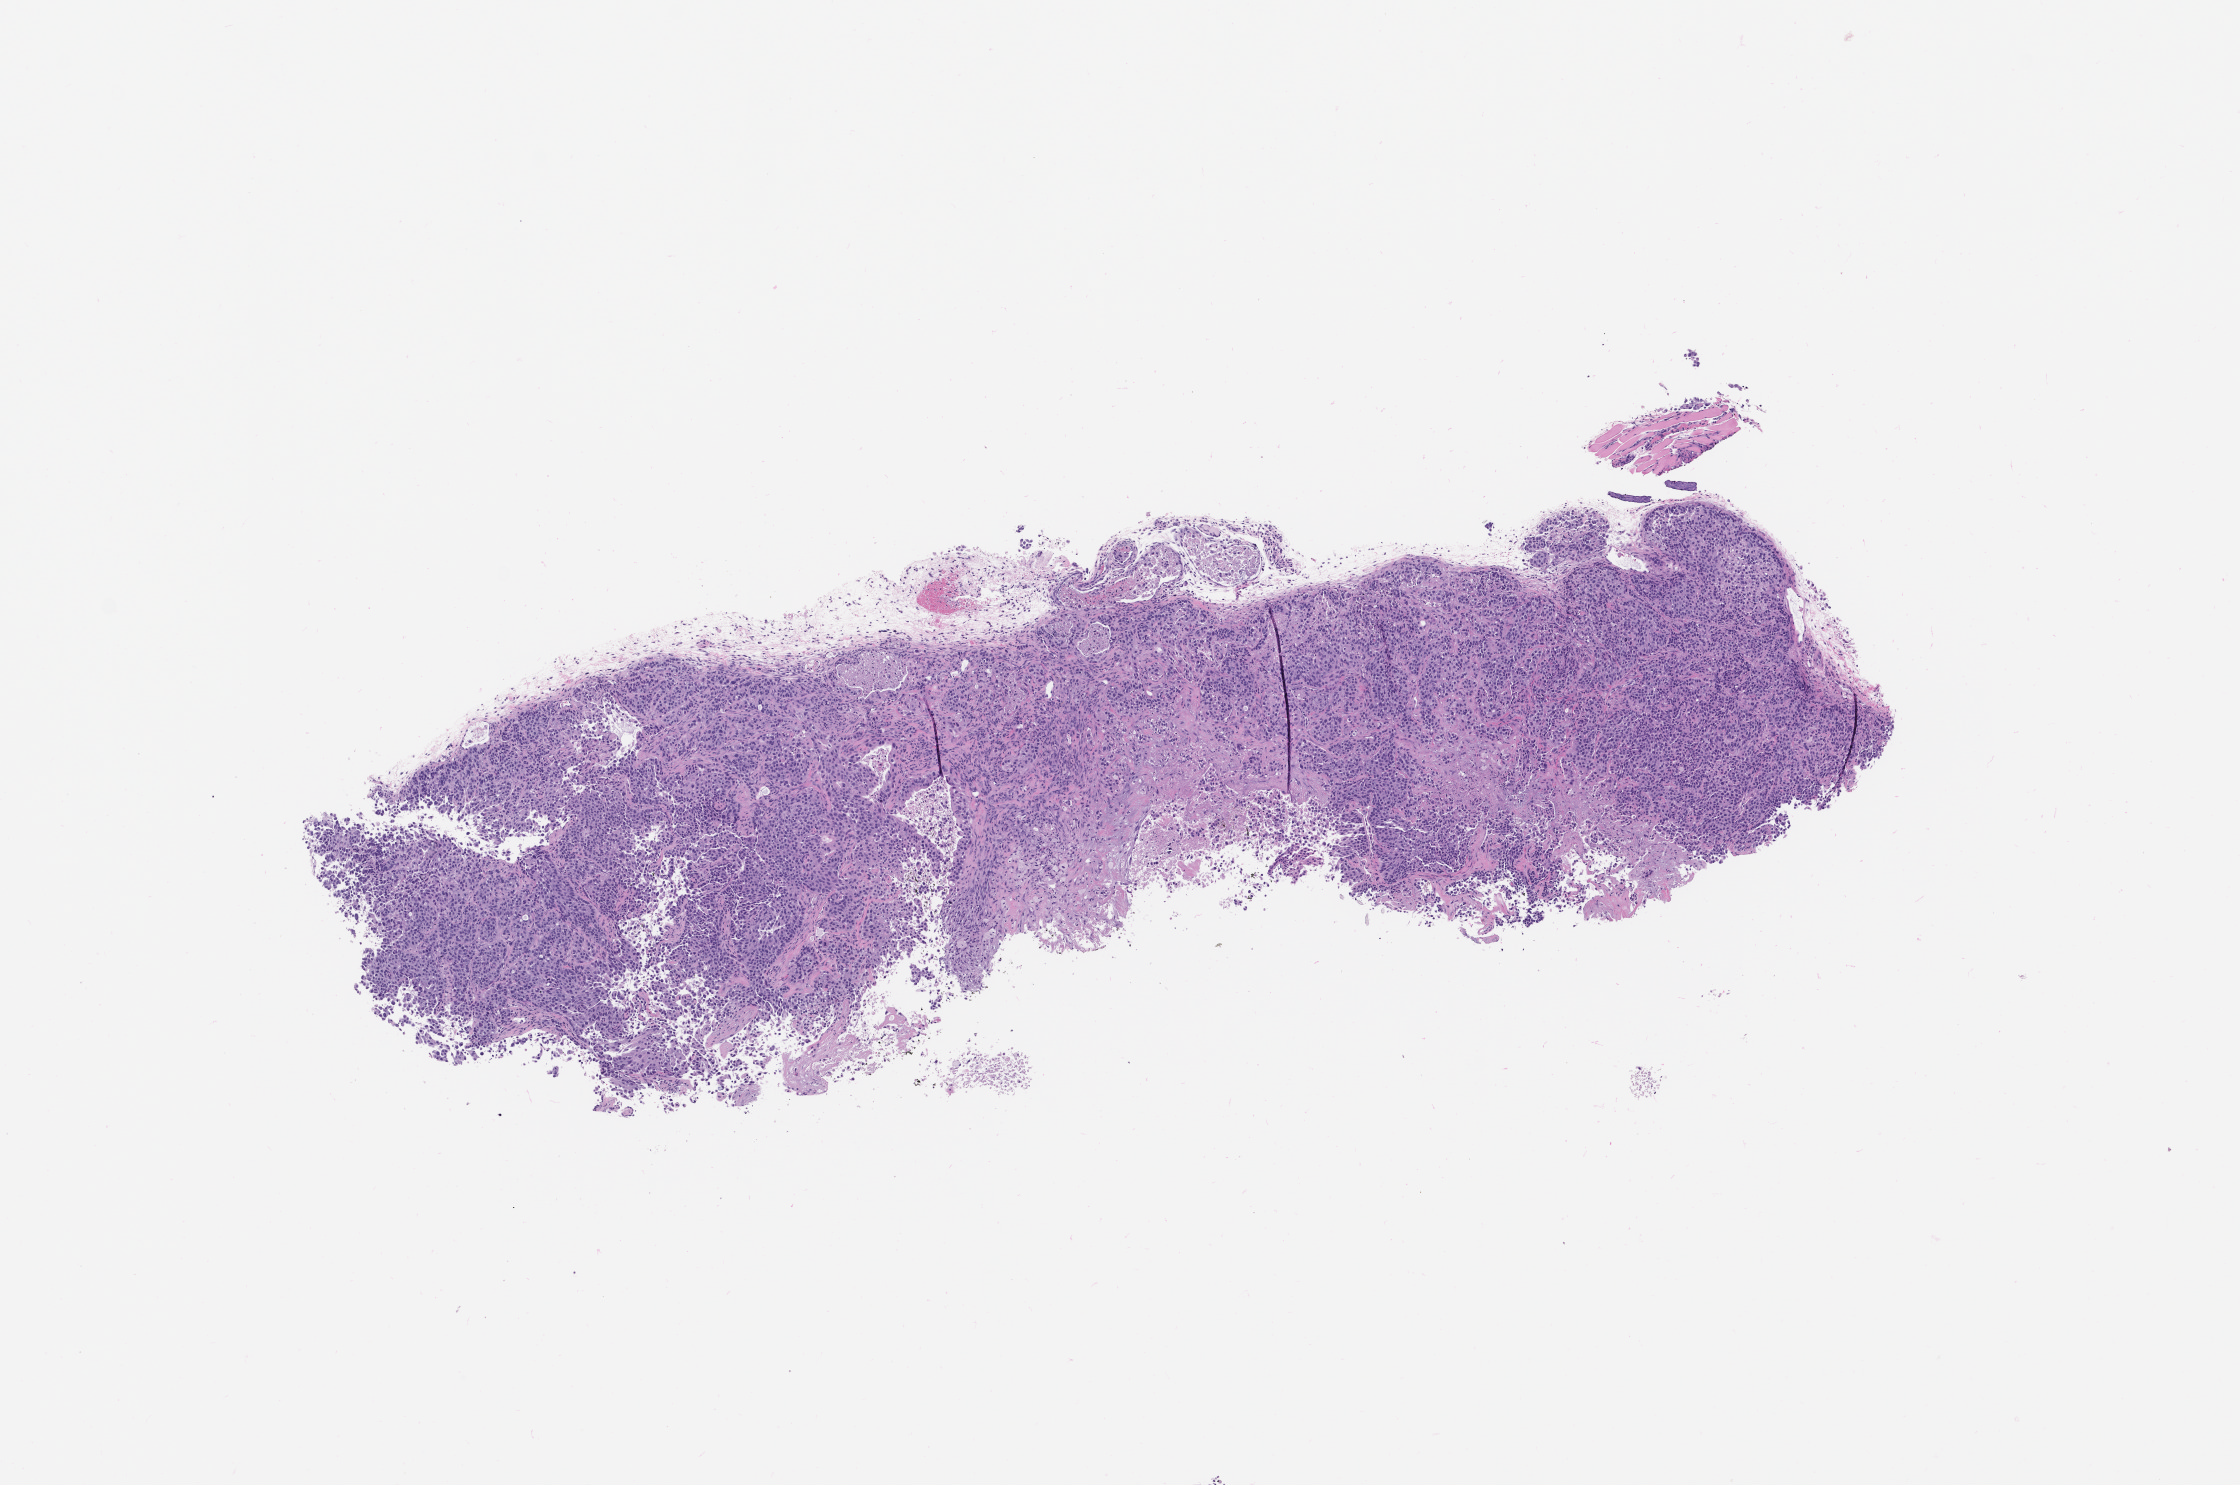
Whole-slide image, H&E: patient-derived xenograft (human tumor grown in a mouse), passage 0 — low-resolution overview of the scanned area, about 9.0 x 5.9 mm; FFPE section; originating tumor site category: bladder.
Originating patient diagnosis: Urothelial Carcinoma.